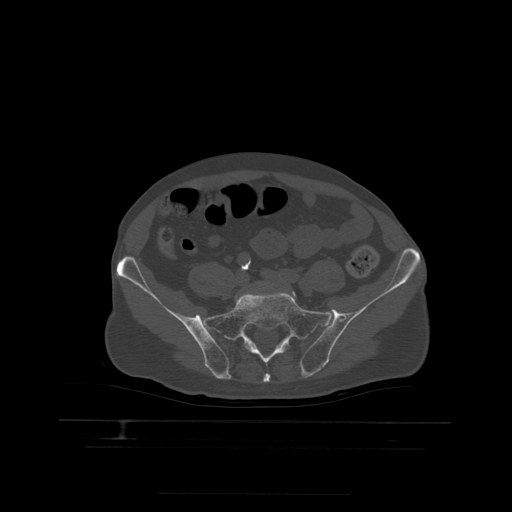
CT including the spine, one axial slice; slice 52 of 522 in the series (ordered by position); bone window (W 1800 / L 400 HU); 1.25 mm slice thickness; 512 × 512 image matrix, field of view 436 × 436 mm. Patient age 68 years. Case-level facts recorded for this patient, not image findings: primary cancer: urothelial.
Structures marked on this image (semi-automatically segmented with operator editing):
- L5 vertebra: bounding box <292,291,297,298> (left, top, right, bottom; pixels)